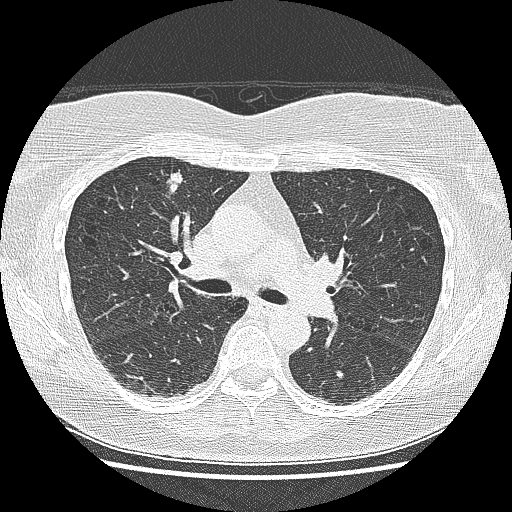
Low-dose screening chest CT, one axial slice; slice 93 of 155 in the series (ordered by position); lung window (W 1500 / L -600 HU); 2.5 mm slice thickness; 512 × 512 image matrix.
Annotated regions visible in this slice (outlined manually by an expert reader):
- lesion 1 (tumor, upper lobe of right lung): box from (x=167, y=170) to (x=183, y=193) px